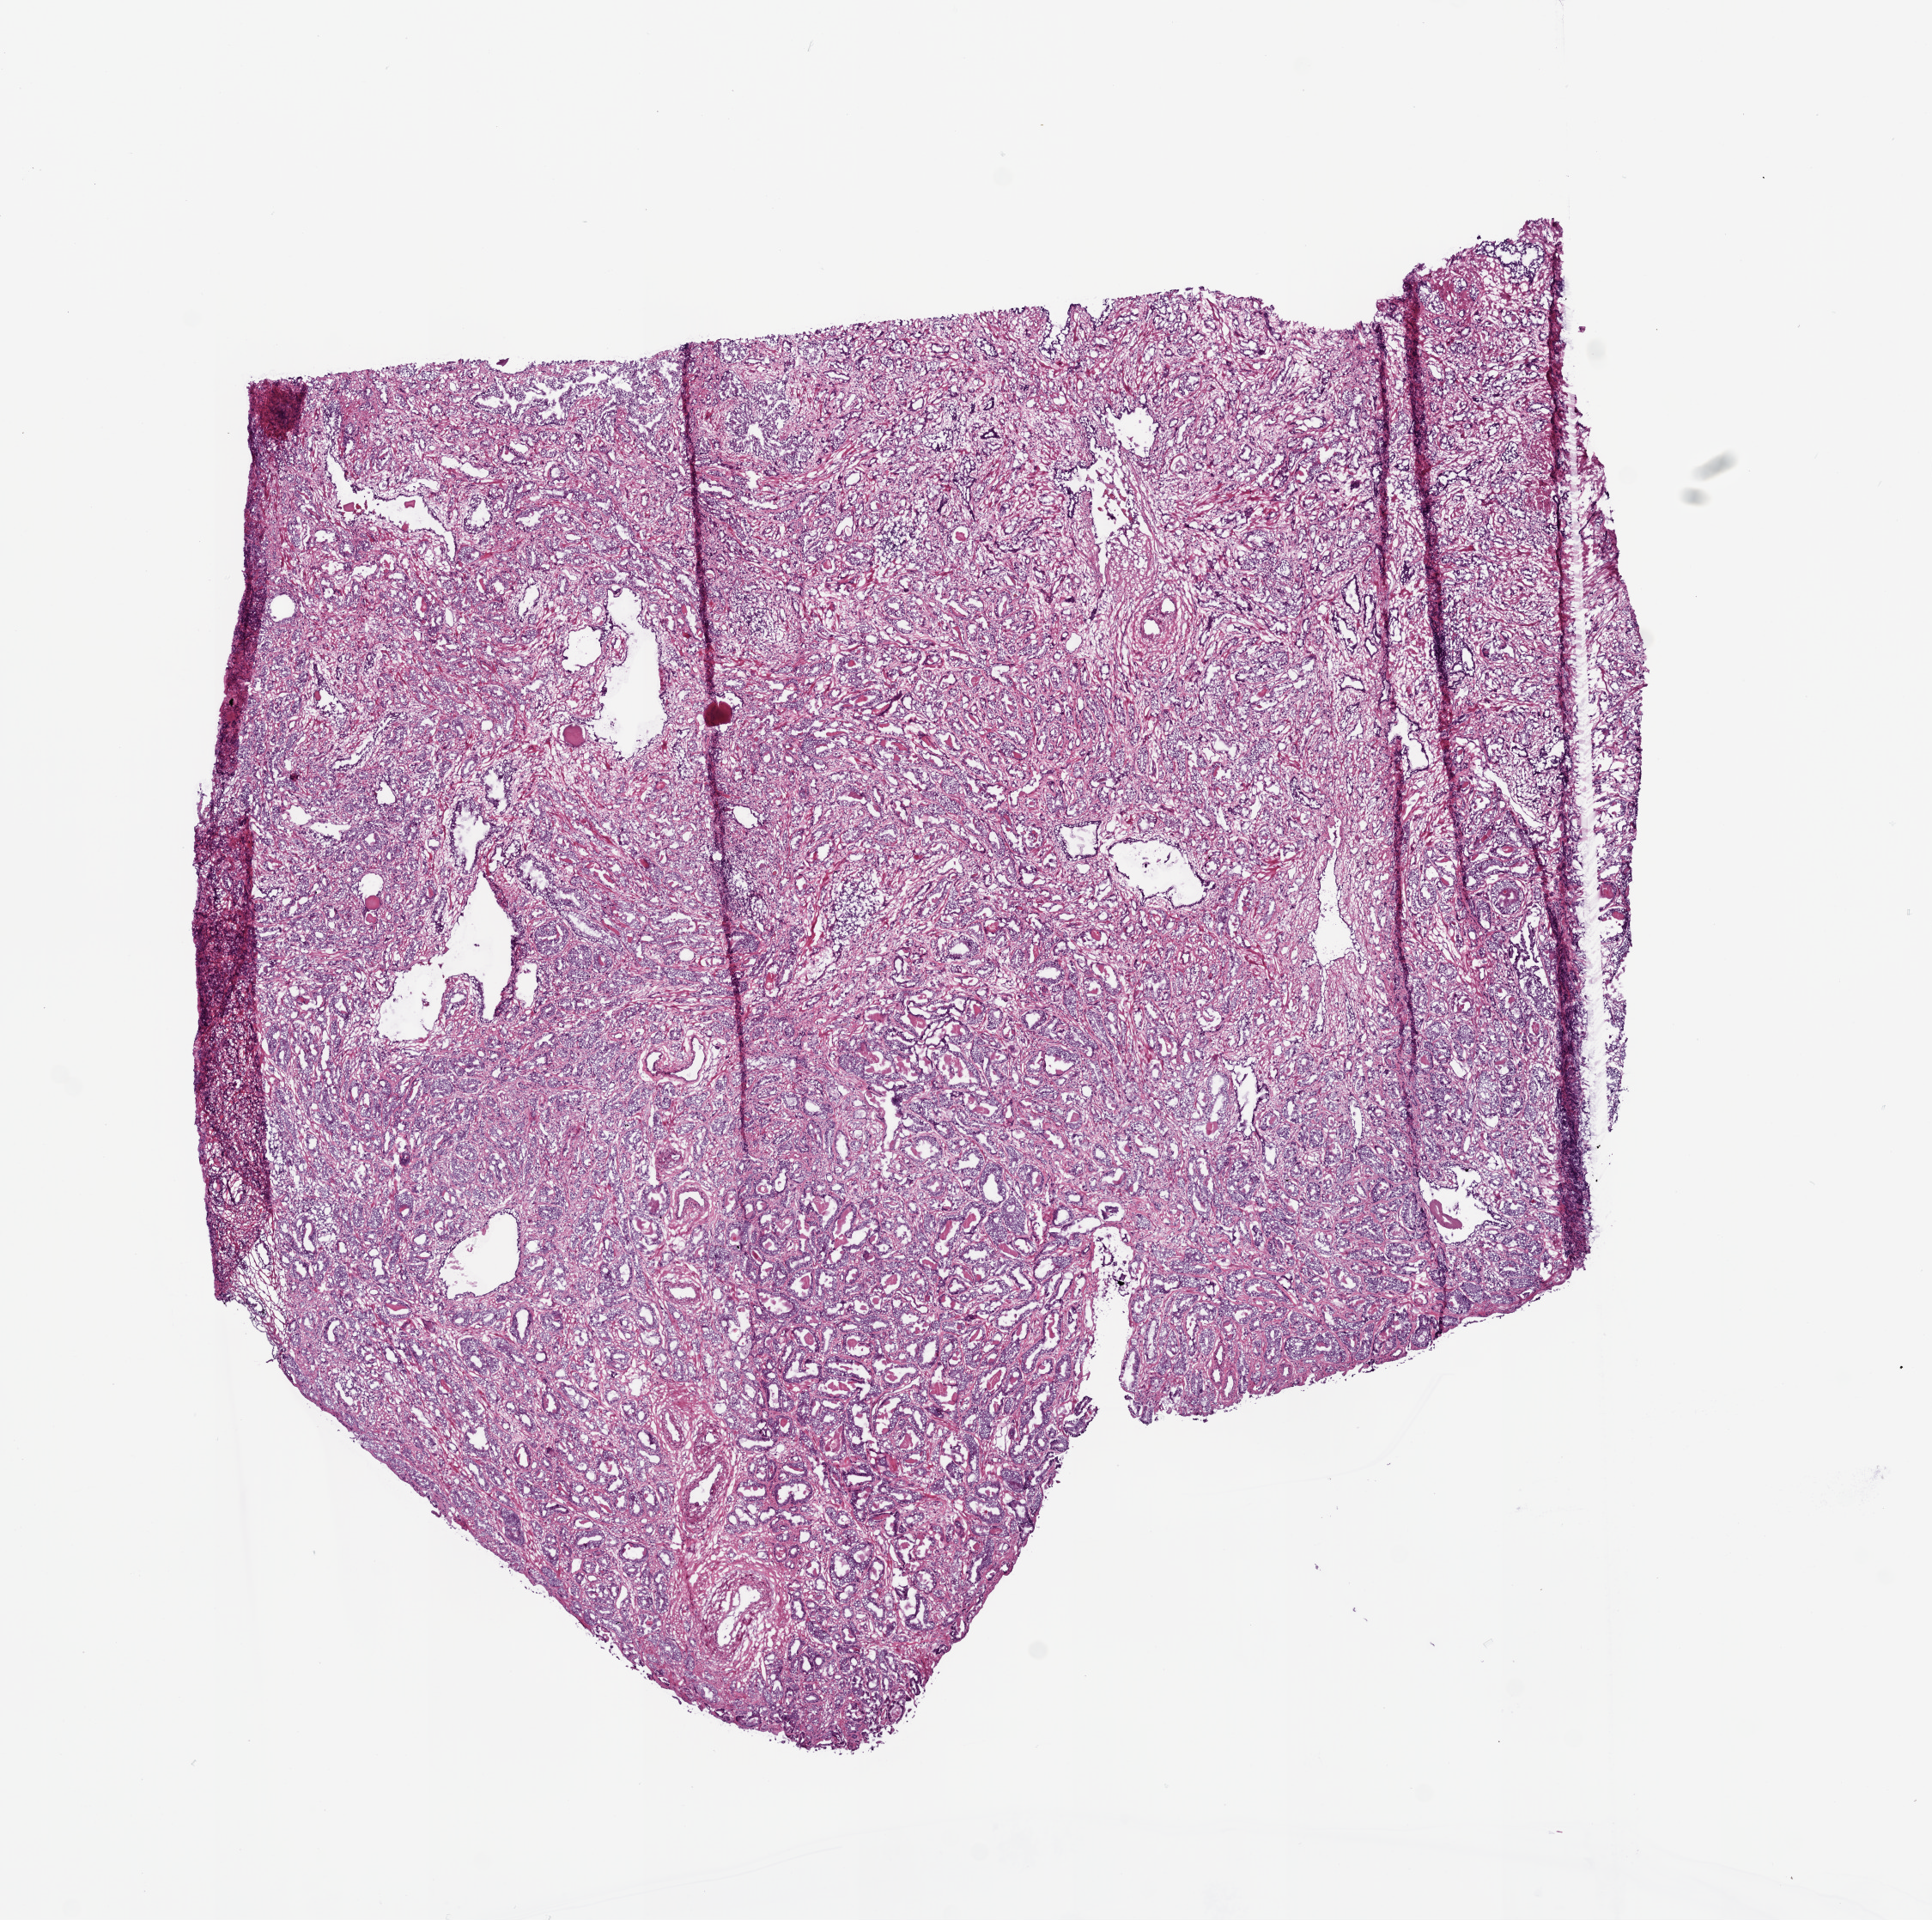
Digitized H&E-stained tissue section (whole slide), whole scanned area (about 9.0 x 9.0 mm, from a 20x scan) shown as a low-resolution overview. Frozen section from the top of the tissue portion. Prostate, primary tumour sample. Male, age 63 years at initial diagnosis. Gleason score: 7 (3+4). Composition of this section per pathologist review: tumour cells 75%, tumour nuclei 80%, normal cells 10%, stromal cells 15%, necrosis 0%. Inflammatory infiltration, as recorded: lymphocyte infiltration 2%, monocyte infiltration 0%, neutrophil infiltration 0%.
Histologic diagnosis: Acinar cell carcinoma (prostate gland). Lymph nodes positive (case pathology): 0 of 10 examined.